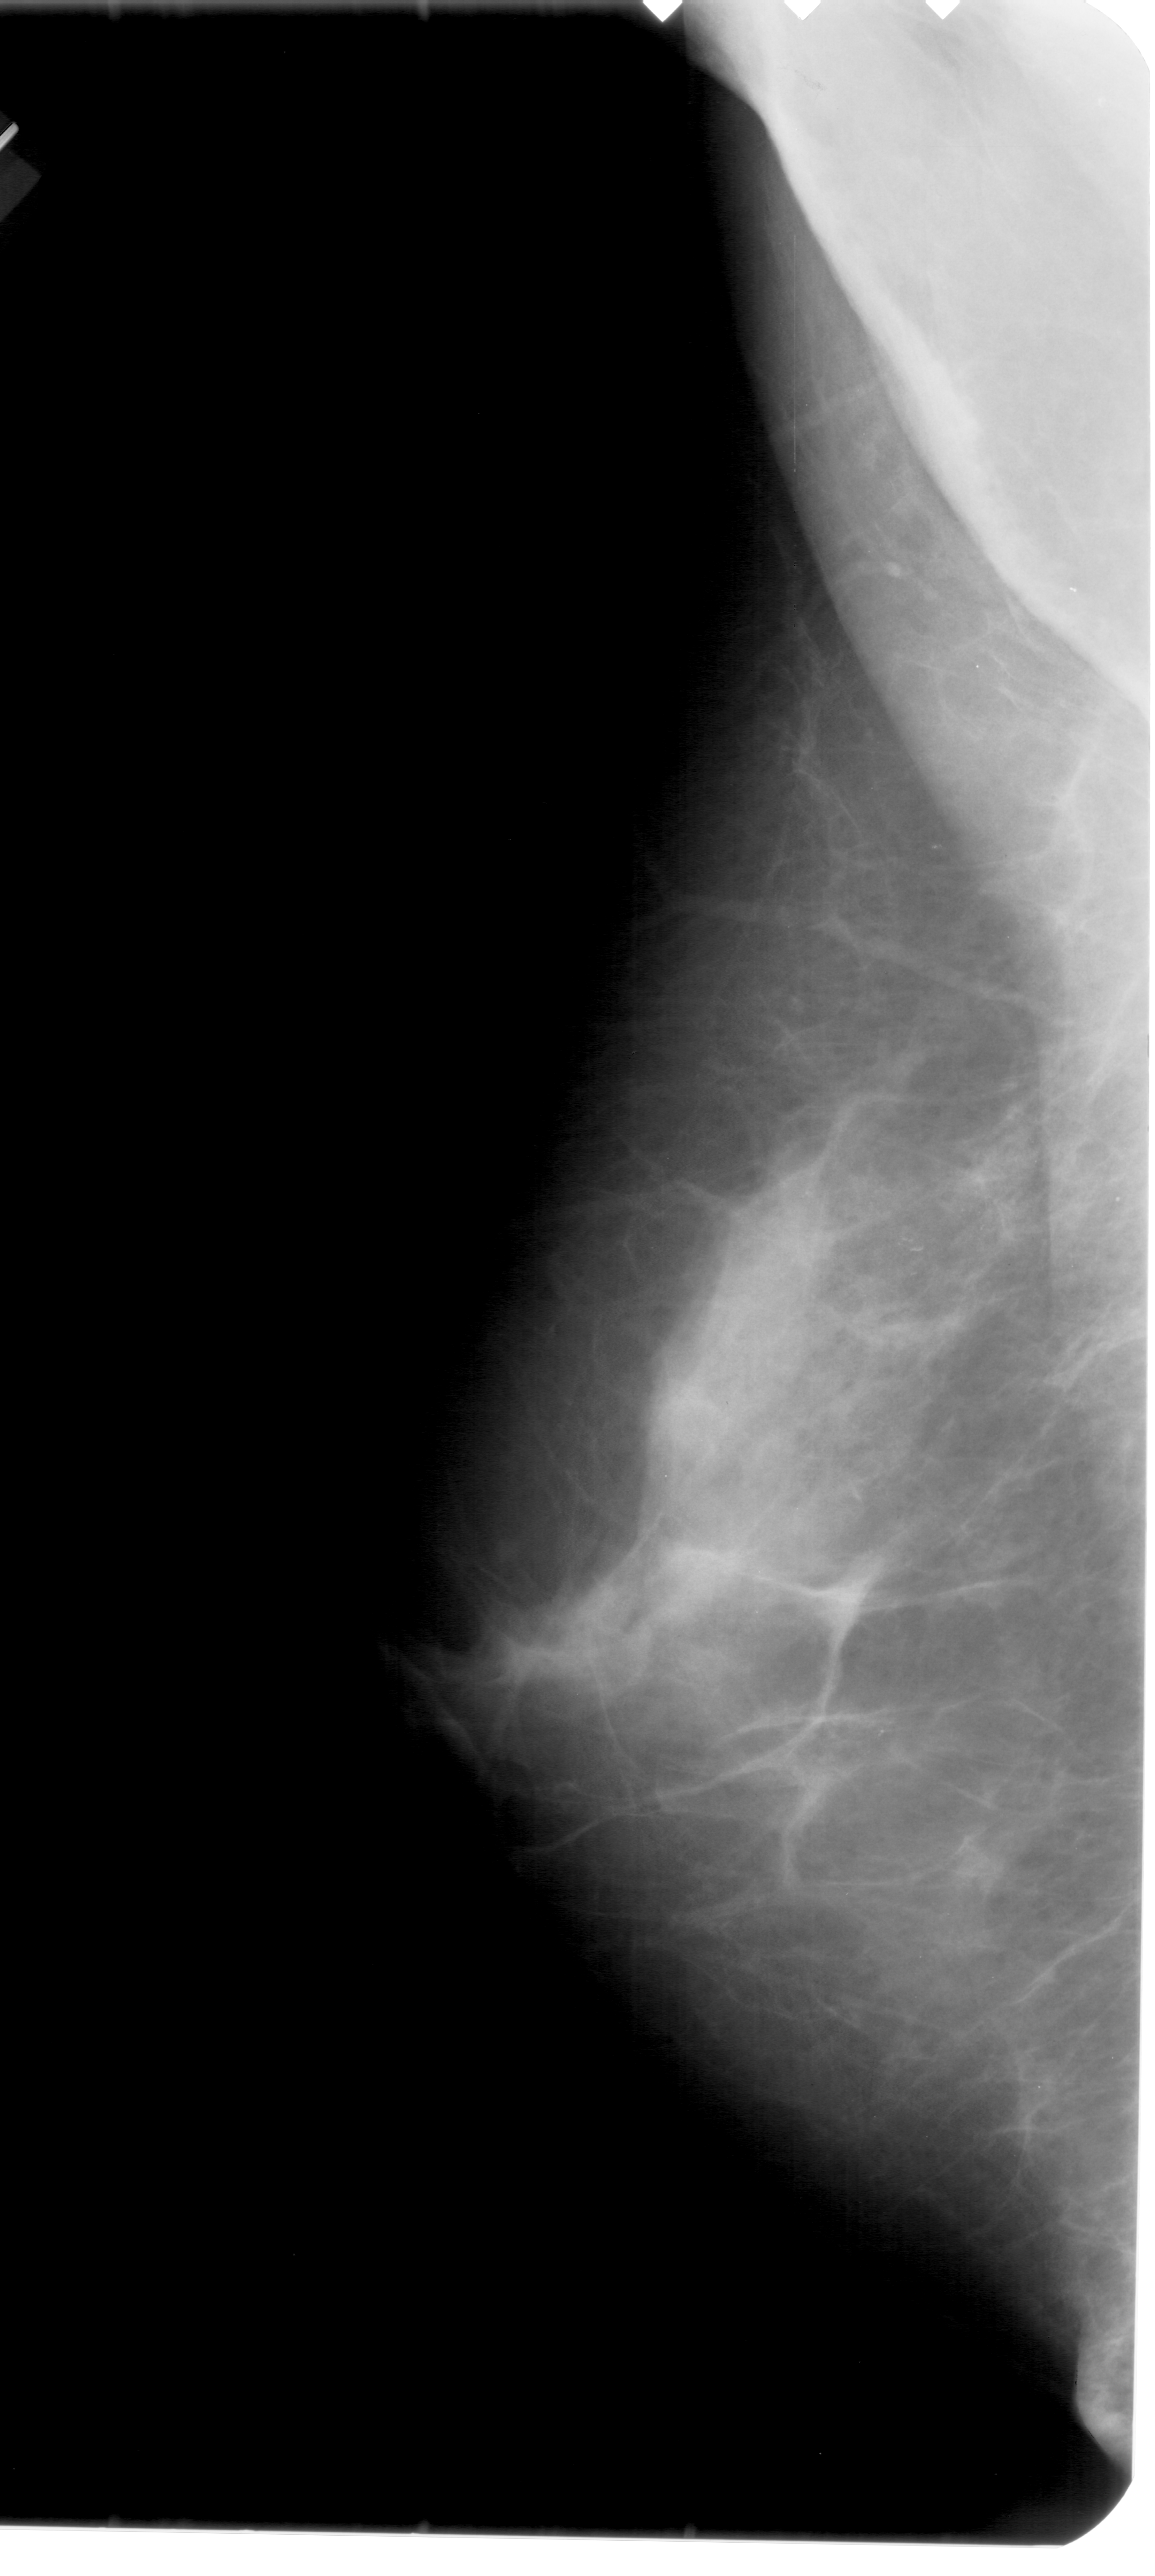
Mammogram (digitized film); left breast; mediolateral oblique (MLO) view; breast composition: extremely dense (BI-RADS density category 4 of 4).
Marked findings (only marked abnormalities are described; nothing is implied about the rest of the image): calcifications, morphology pleomorphic, distribution clustered; BI-RADS assessment category 4; pathology (as recorded): benign.